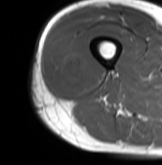
MRI of an extremity soft-tissue mass, one axial slice. Slice 25 of 61 in the series (ordered by position). MR volume resampled by the dataset authors to the PET/CT grid (not the native acquisition matrix). 162 × 165 image matrix. Male patient. From the clinical record (not read from this slice): histological type: poorly differentiated synovial sarcoma; grade: high; site of the primary tumour: right buttock.
Annotated regions visible in this slice (expert contour drawn on MRI and transferred to this co-registered scan by the dataset authors):
- gross tumour volume including surrounding oedema: bounding box (x1, y1, x2, y2) in pixels: (50, 40, 104, 96)
- gross tumour volume (mass): (52, 42, 90, 92)